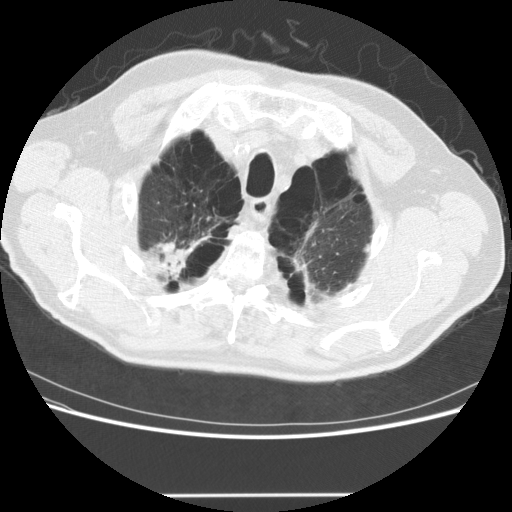
Low-dose screening chest CT, axial slice. Third screening round (two years after baseline). Lung window (W 1500 / L -600 HU). 2.5 mm slice thickness. Standard (soft-tissue) reconstruction kernel (STANDARD). 120 kVp. 512 × 512 image matrix, field of view 360 × 360 mm. Male participant, aged 68 years at enrolment. Former smoker at enrolment.
• Lesion marked by an expert reader, bounding box <130,214,215,290> (left, top, right, bottom; pixels).
• The screening reader recorded 2 non-calcified nodules or masses ≥4 mm on this exam (lingula, left lower lobe); which of them this box marks is not recorded.
• Official screen result: positive, no significant change: stable abnormalities potentially related to lung cancer, unchanged since the prior screening exam.